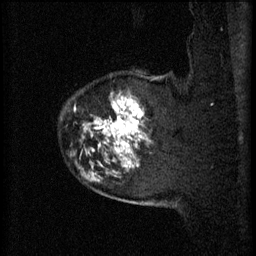
Breast MRI (dynamic contrast-enhanced), one sagittal slice; position 53 of 60 along the scan axis; 3 images stored at this slice position (order not interpretable as contrast timing); 1.5 T; TE 4.2 ms, TR 11 ms; 2 mm slice thickness; 256 × 256 image matrix, field of view 180 × 180 mm. Patient: female, 52 years.
Annotated regions visible in this slice (semi-automatically segmented with operator editing):
- analysis volume of interest (the breast-tissue region the enhancement analysis was run in; not a lesion): box from (x=83, y=70) to (x=163, y=157) px
- tumour enhancement mask (voxels above the 70 % enhancement threshold inside the analysis volume of interest): (x=84, y=98)–(x=145, y=157)